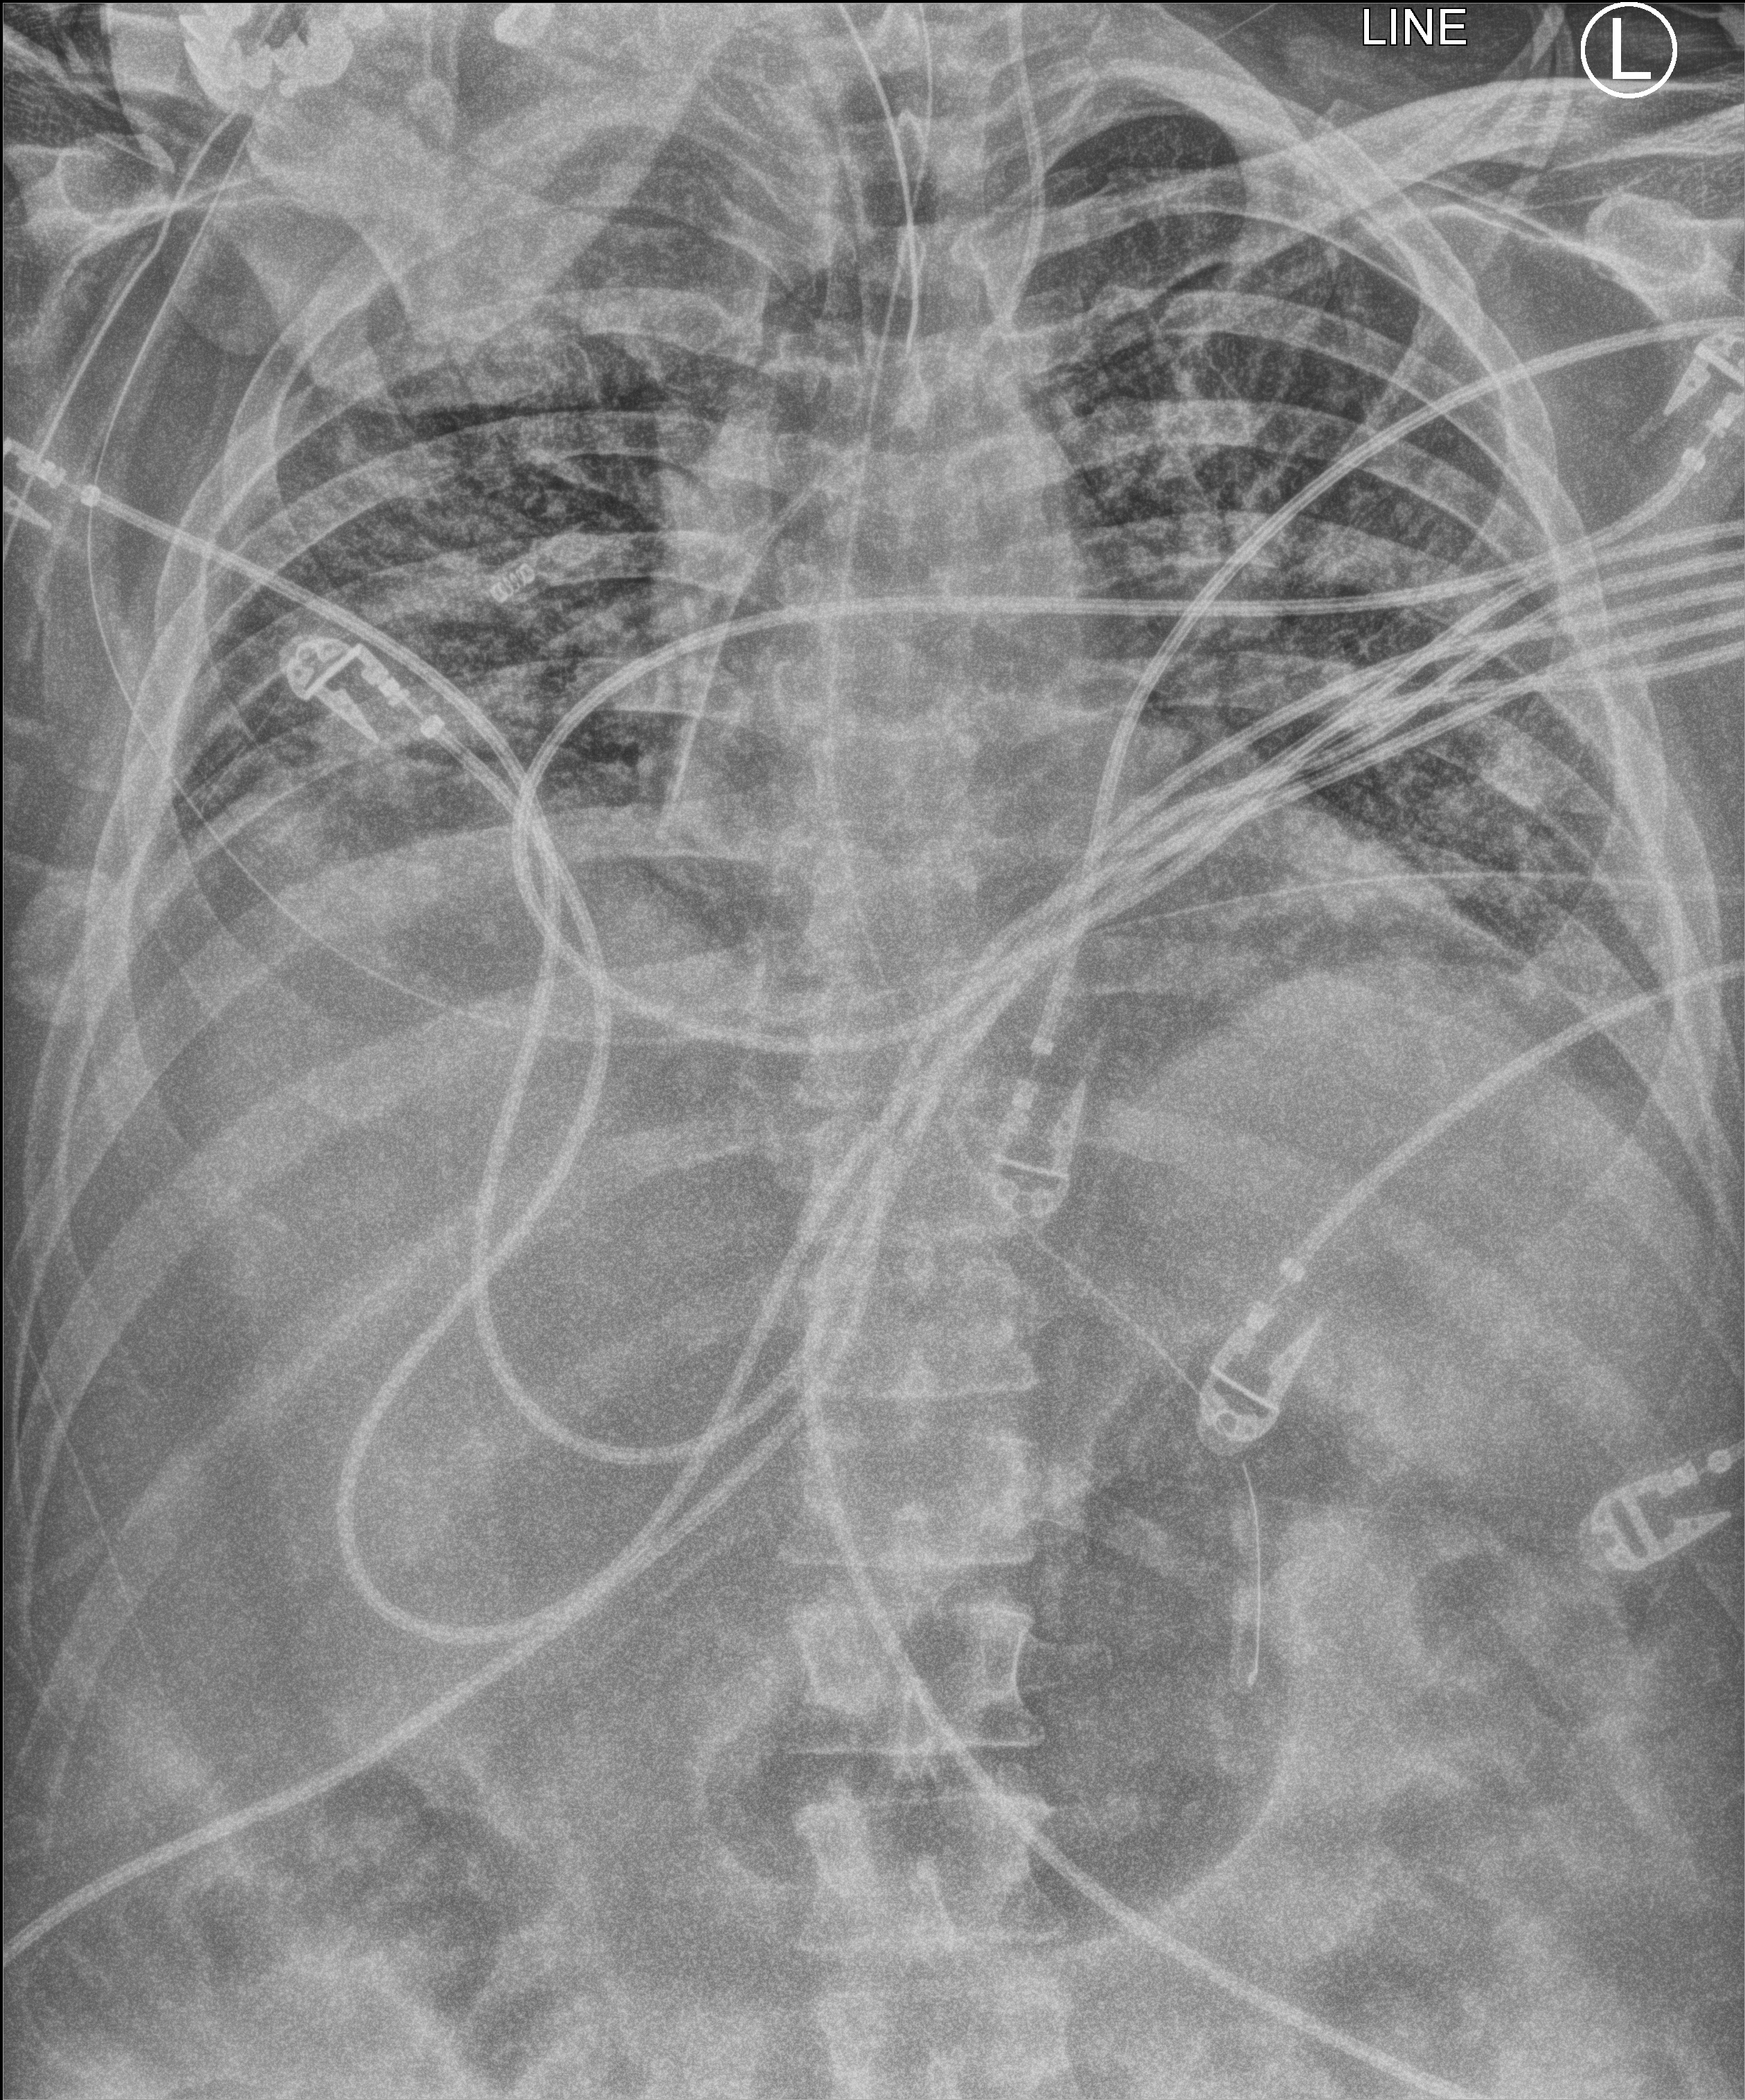
Bedside chest radiograph (computed radiography), anteroposterior (AP) projection. Male patient hospitalised with COVID-19, age 18–59 years.
Hospital-stay facts (about this admission, not read from this image; timing relative to this image not recorded):
- admitted to intensive care during this hospital stay: yes
- length of hospital stay: 80 days
- mechanically ventilated during this hospital stay: yes